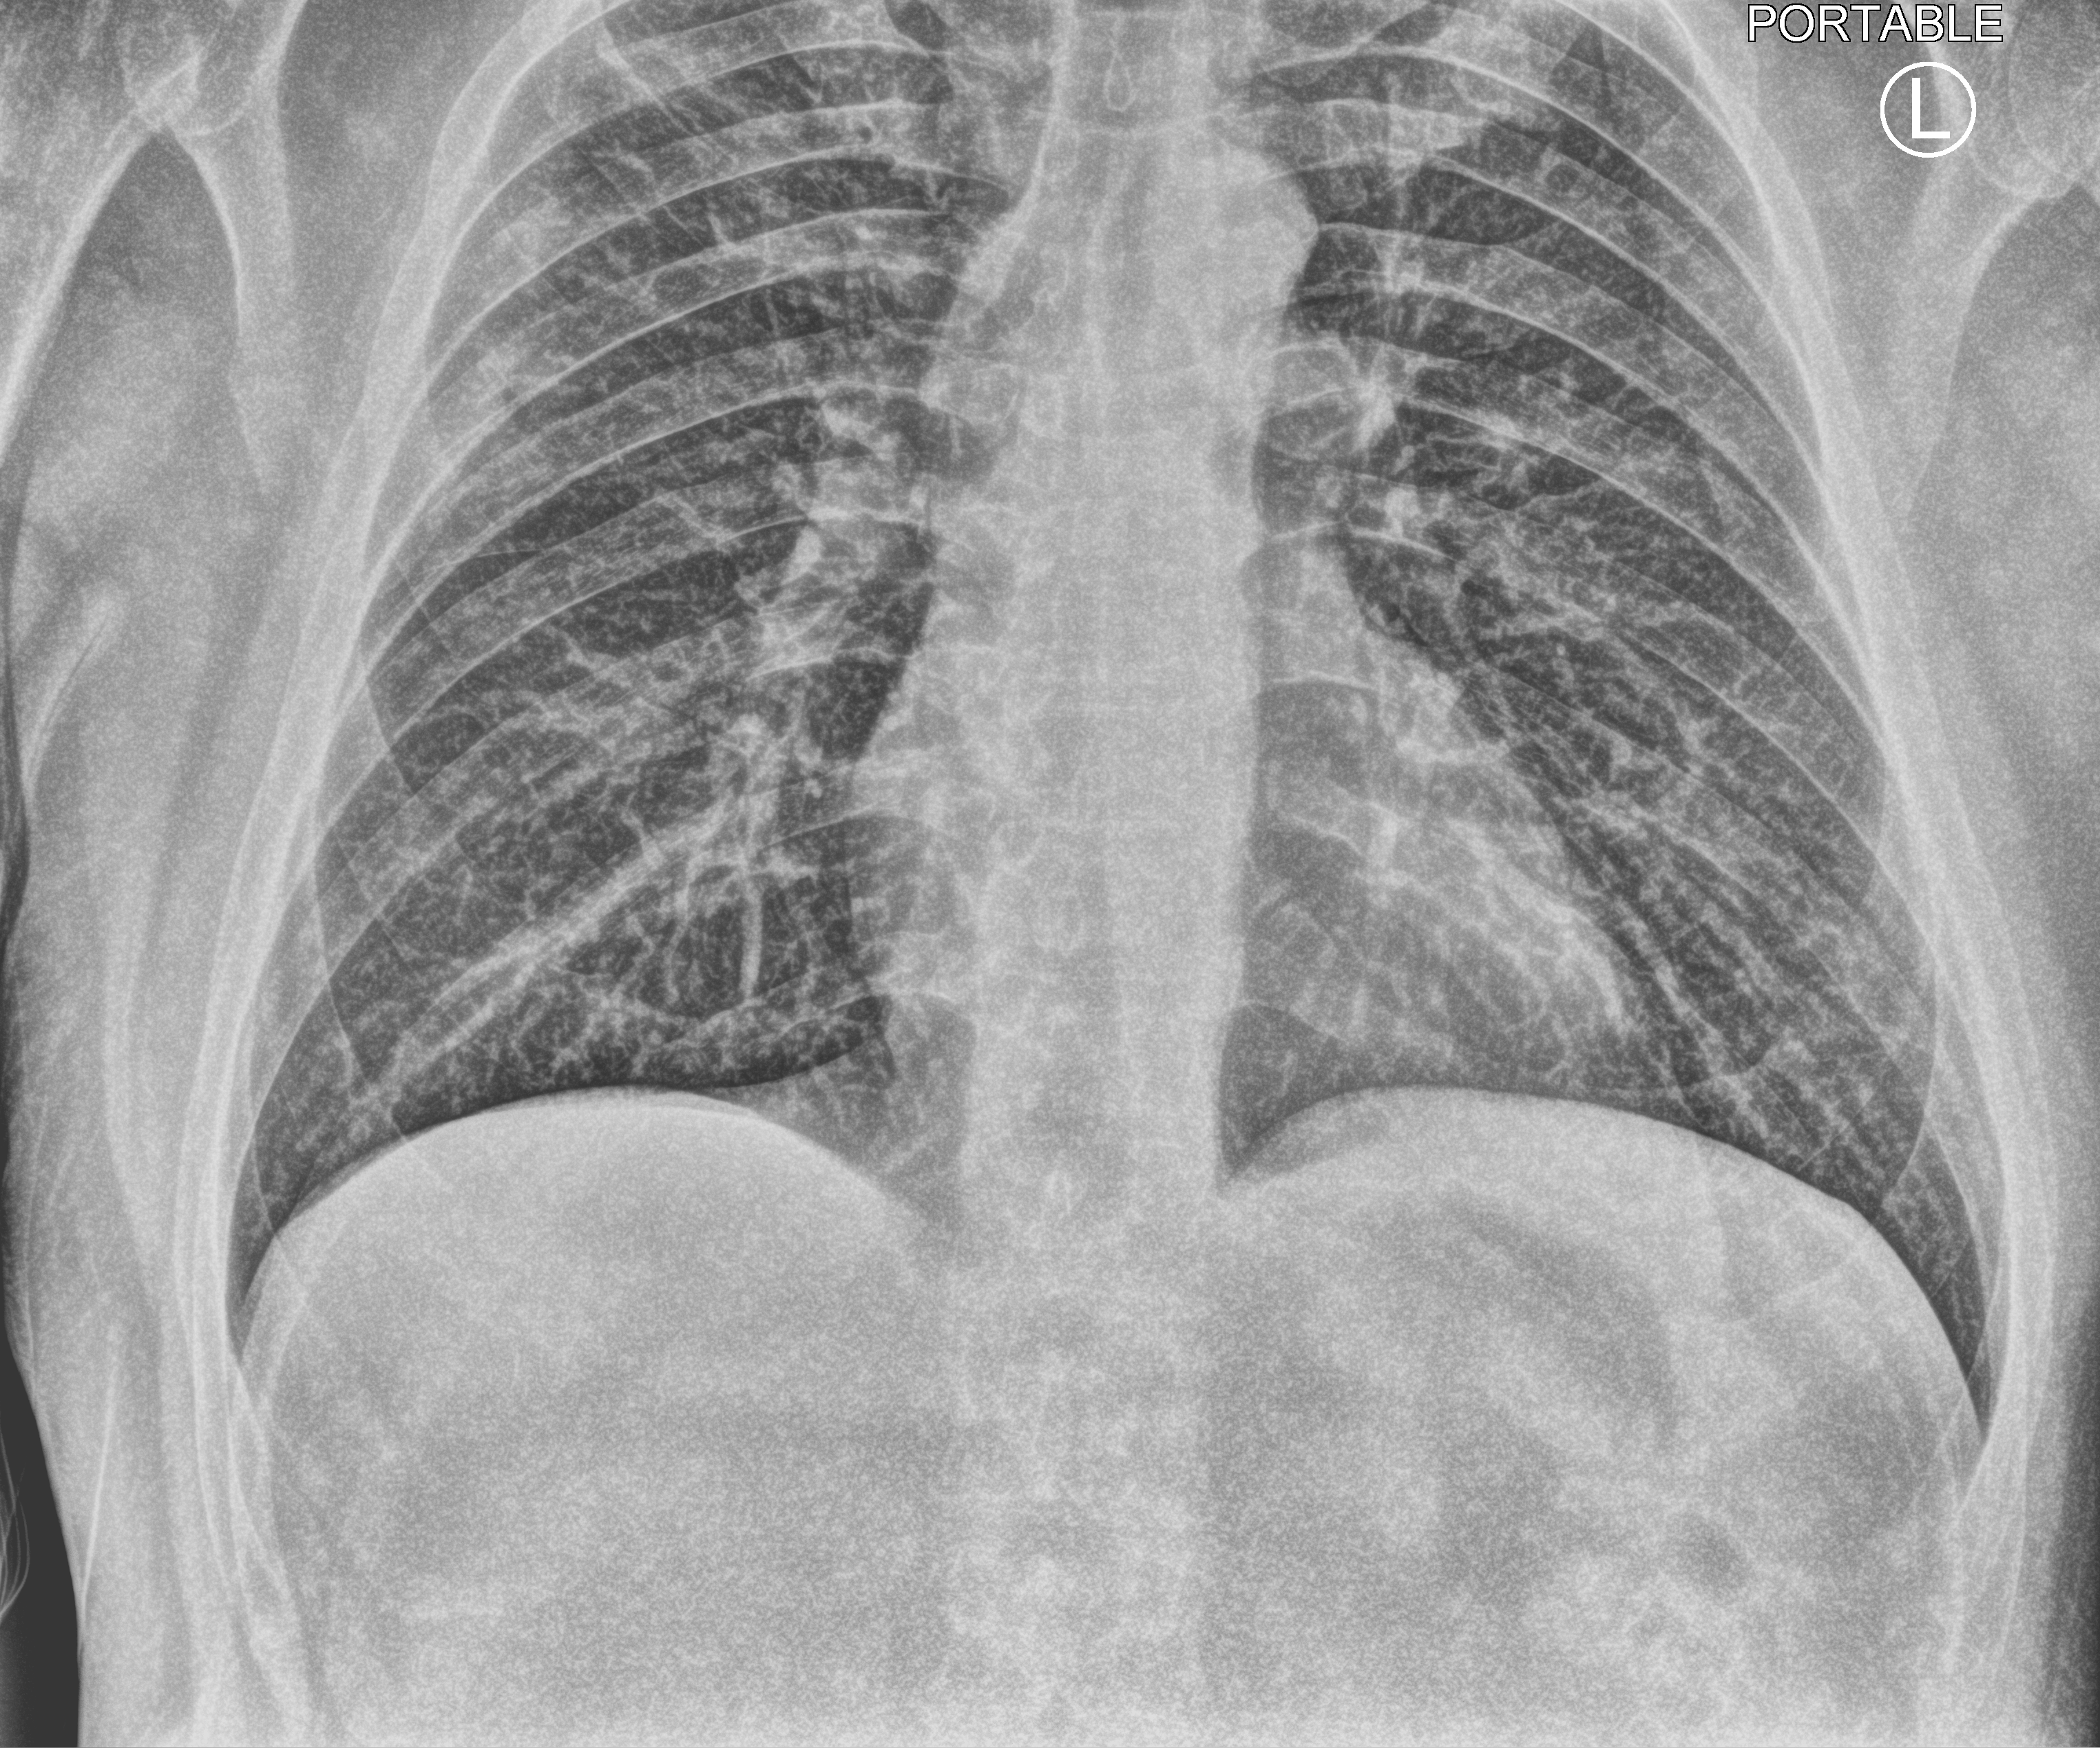
Bedside chest radiograph (computed radiography). Patient hospitalised with COVID-19; male, aged 18–59 years.
From the hospital-stay record, not from the radiograph (when in the stay this image was taken is not recorded): admitted to intensive care during this hospital stay: no.